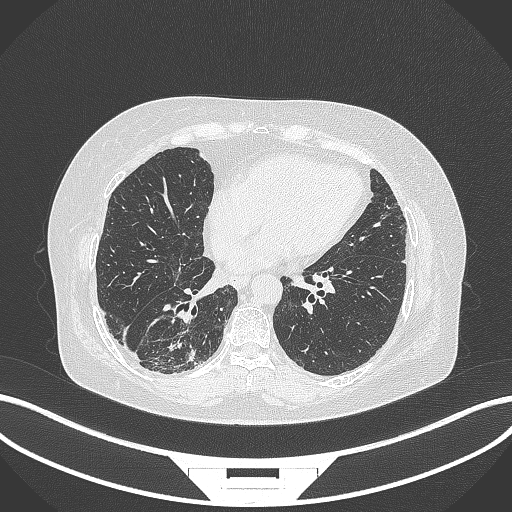
Chest CT, one axial slice. Slice 83 of 296 in the series (ordered by position). Reconstruction kernel B70f. Lung window (W 1500 / L -600 HU). 1 mm slice thickness. 512 × 512 image matrix, field of view 400 × 400 mm. Patient: female, 65 years. Case-level facts recorded for this patient, not image findings: clinical TNM (as recorded): T2b N1 M0; histopathological grade: G1.
Annotated regions visible in this slice (bounding box drawn by a radiologist):
- lung tumour (recorded histology: adenocarcinoma): bounding box (x1, y1, x2, y2) in pixels: (137, 309, 196, 373)